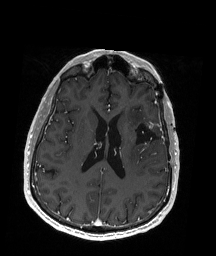
Brain MRI from a brain-tumour surgery series, one axial slice. Position 81 of 192 along the scan axis. T1-weighted post-contrast. 1 mm slice thickness. 216 × 256 image matrix, field of view 211 × 250 mm. From the clinical record (not read from this slice): histopathology: Oligodendroglioma; WHO grade: 2; IDH mutation: yes; tumour location: Left Insular.
Structures marked on this image (outlined manually by an expert reader):
- previous resection cavity: bounding box <132,121,163,148> (left, top, right, bottom; pixels)